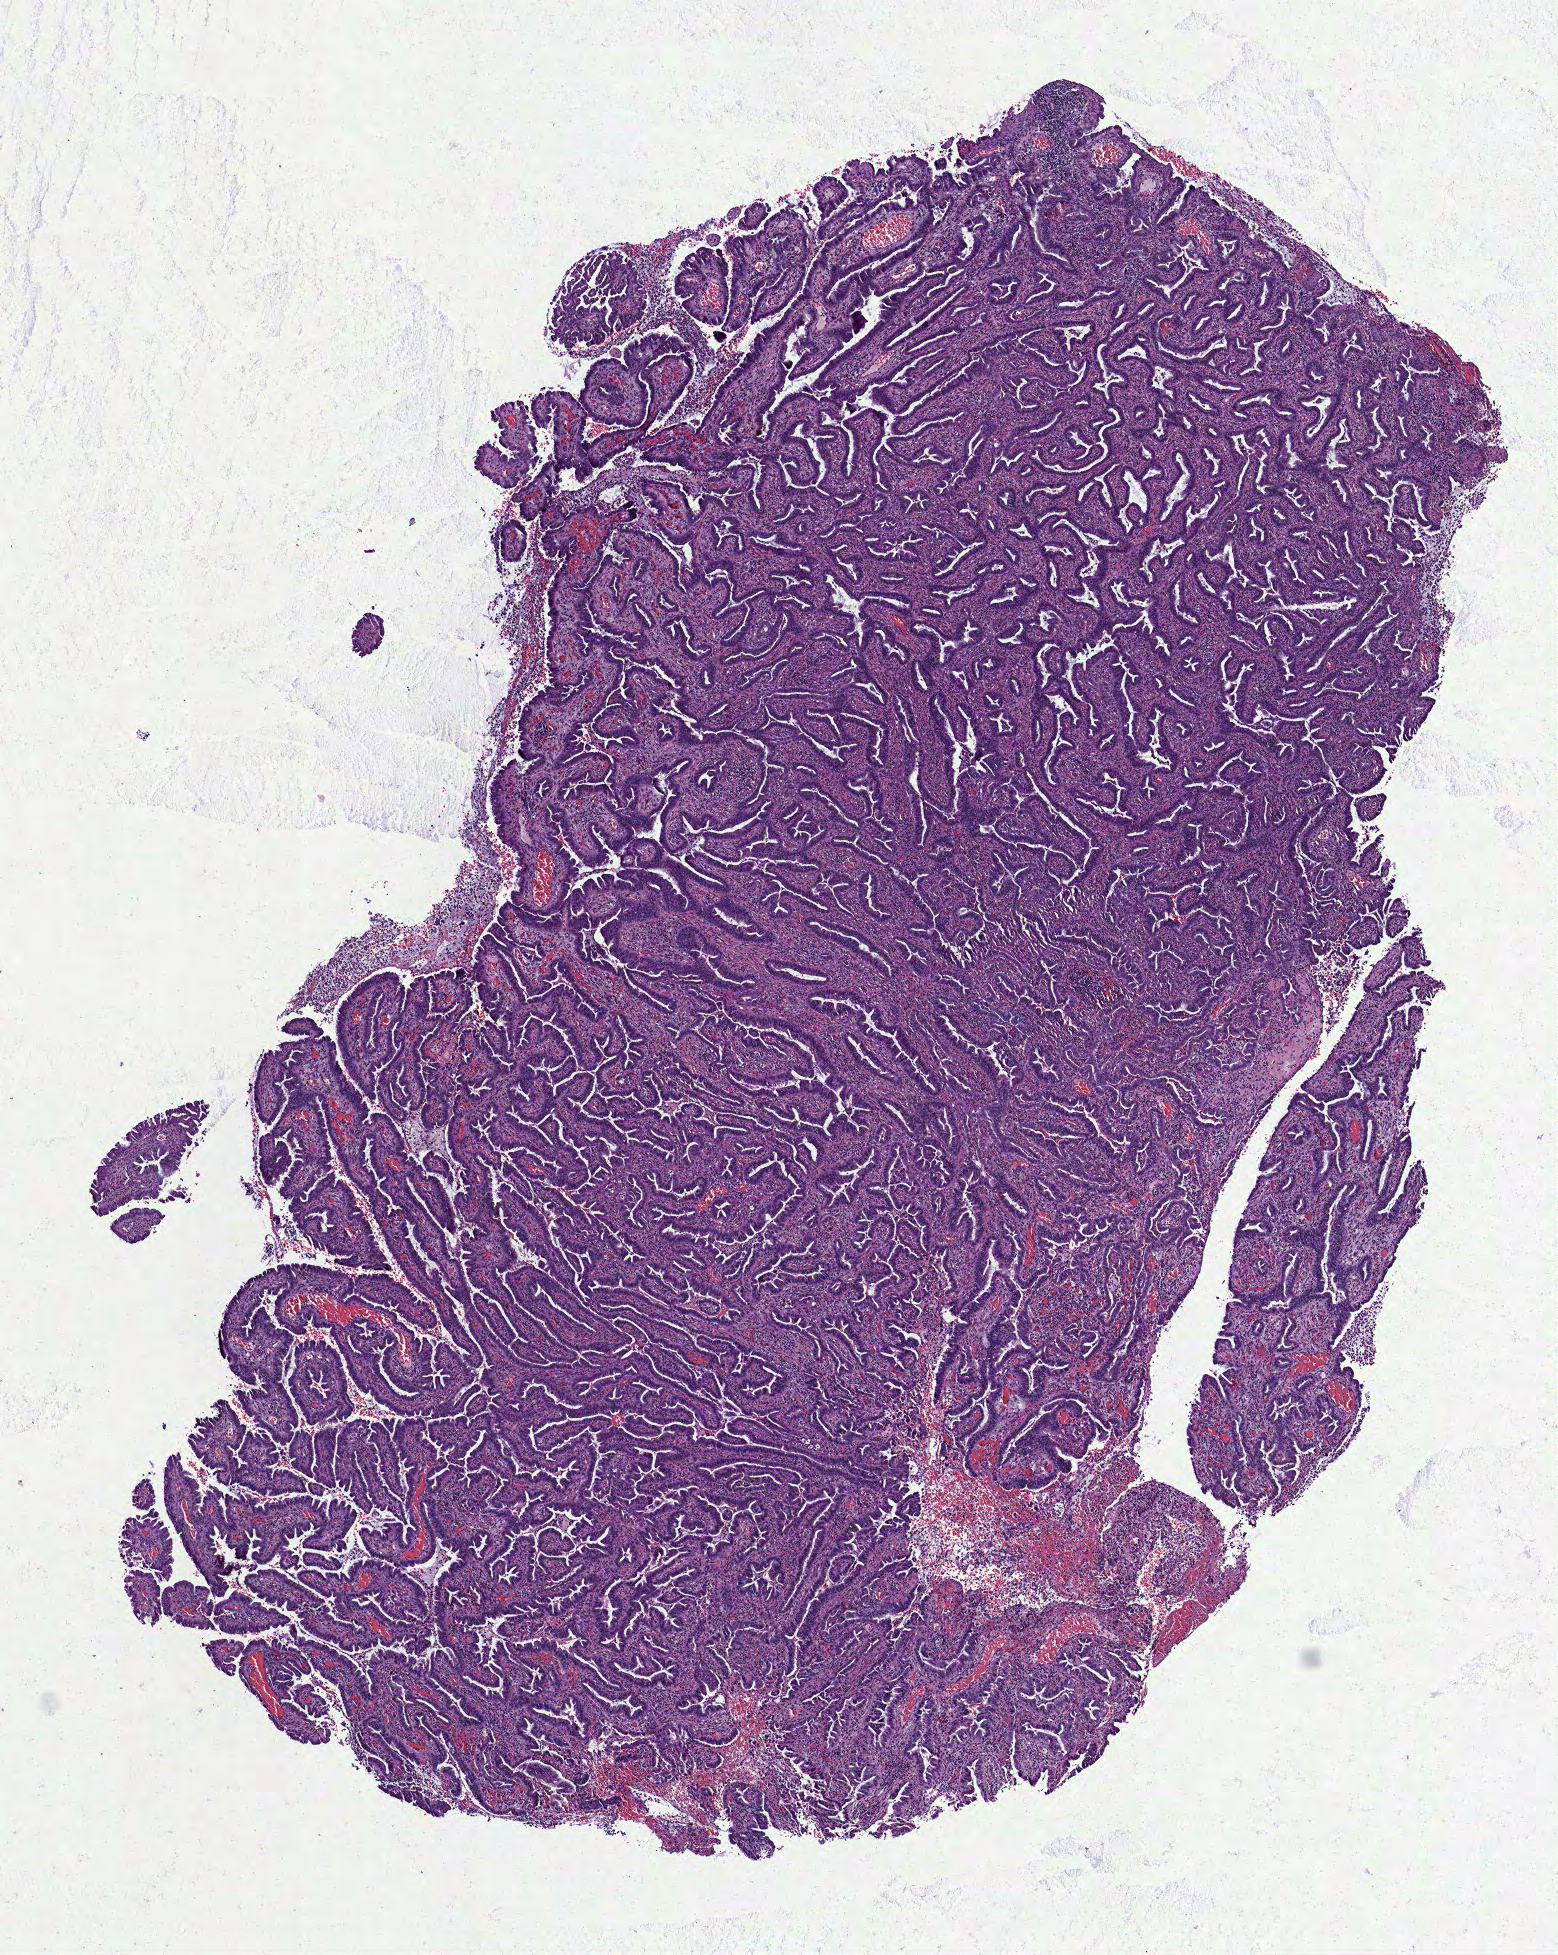
Digitized H&E-stained tissue section (whole slide) — shown as a low-resolution overview of the whole scanned area (about 6.3 x 7.9 mm), formalin-fixed paraffin-embedded (FFPE) diagnostic section, sample: primary tumour, cervix. Female patient; age at initial diagnosis 33 years. Histologic grade: G2 (moderately differentiated).
- histologic diagnosis: Adenocarcinoma, endocervical type
- lymph nodes positive (case pathology): 1 of 10 examined
- FIGO stage: IIIB